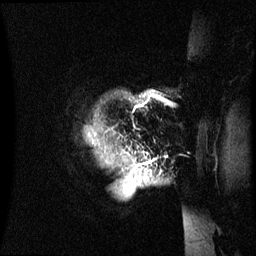
Breast MRI (dynamic contrast-enhanced), one sagittal slice; slice 59 of 60 in the series (ordered by position); dynamic contrast-enhanced series, image 2 of 3 at this slice position (ordered by acquisition); 1.5 T; TE 4.2 ms, TR 8.4 ms; 256 × 256 image matrix. Patient: female, 48 years.
Structures marked on this image (semi-automatic segmentation, software-assisted and operator-edited):
- analysis volume of interest (the breast-tissue region the enhancement analysis was run in; not a lesion): bounding box <87,90,187,232> (left, top, right, bottom; pixels)
- tumour enhancement mask (voxels above the 70 % enhancement threshold inside the analysis volume of interest): <126,161,151,180>